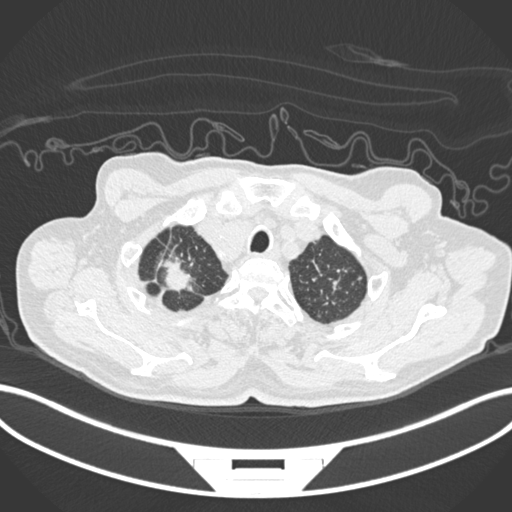
Chest CT, one axial slice. Slice 197 of 207 in the series (ordered by position). Reconstruction kernel B30f. Lung window (W 1500 / L -600 HU). 1 mm slice thickness. 512 × 512 image matrix. Male patient, age 69 years. Case-level facts recorded for this patient, not image findings: clinical TNM (as recorded): T1c N1 M1.
Annotated regions visible in this slice (rectangle marked by the reading radiologist):
- lung tumour (recorded histology: adenocarcinoma): bounding box (x1, y1, x2, y2) in pixels: (156, 256, 195, 299)